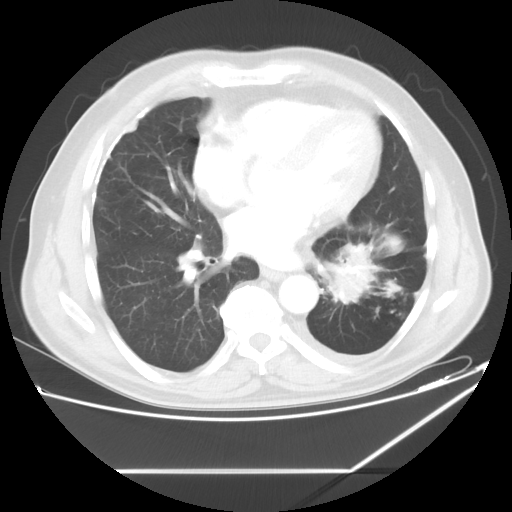
Chest CT, one axial slice; slice 26 of 60 in the series (ordered by position); reconstruction kernel STANDARD; 120 kVp; lung window (W 1500 / L -600 HU); 512 × 512 image matrix, field of view 395 × 395 mm. Male patient, age 62 years. From the clinical record (not read from this slice): clinical TNM (as recorded): T3 N0 M1.
Structures marked on this image (rectangle marked by the reading radiologist):
- lung tumour (recorded histology: adenocarcinoma): bounding box (x1, y1, x2, y2) in pixels: (322, 237, 372, 309)
- lung tumour (recorded histology: adenocarcinoma): (331, 238, 378, 306)